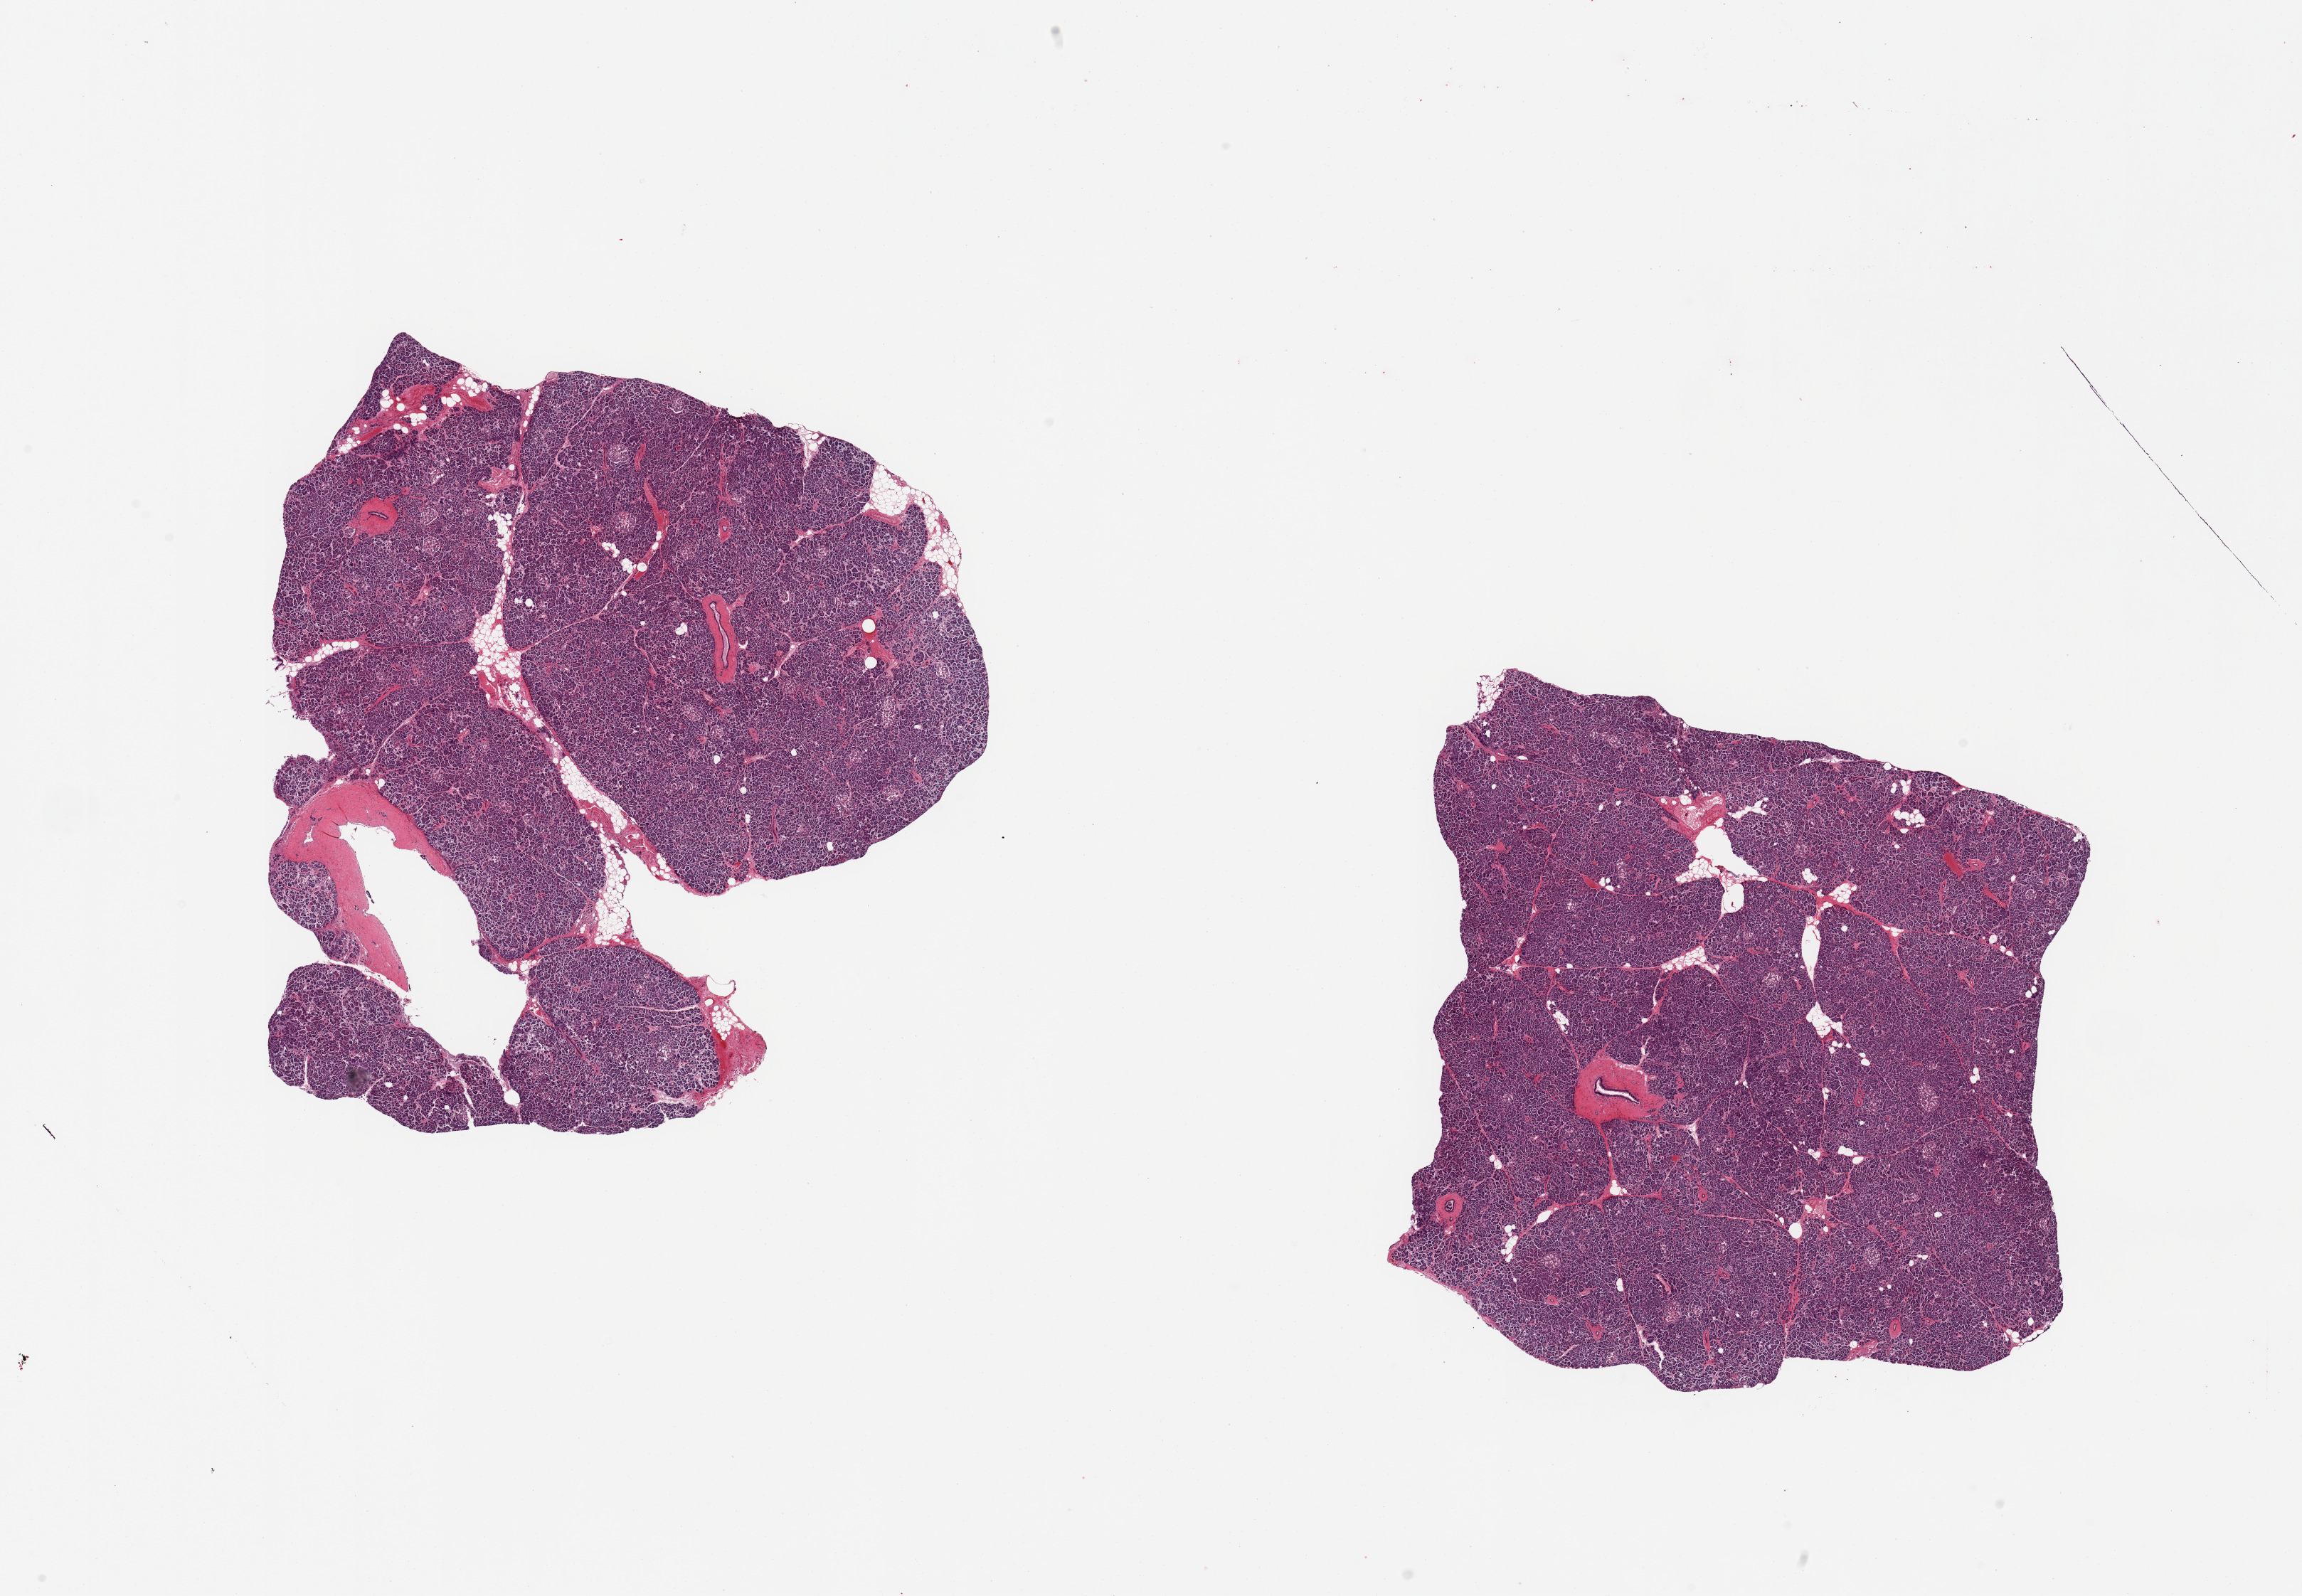
Hematoxylin and eosin (H&E) whole-slide image, brightfield, shown as a low-resolution overview of the whole scanned area (about 25.6 x 17.7 mm, from a 20x scan); PAXgene-fixed, paraffin-embedded tissue; target tissue: pancreas; donor tissue sample. Donor: male.
Reviewer comment on this tissue sample: 2 pieces; well preserevd parenchyma and Langerhans islets; minimal fat.